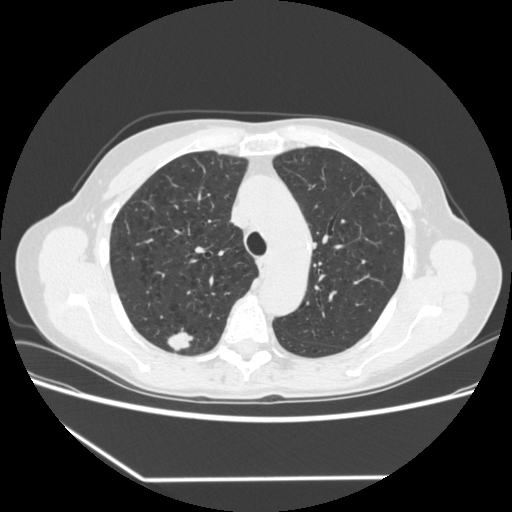
Chest CT (low-dose screening protocol), one axial image. First (baseline) screen. Lung window (W 1500 / L -600 HU). Slice 244 of 323 in the series. 512 × 512 image matrix. Female participant, aged 67 years at enrolment. Current smoker at enrolment.
Expert reader's lesion annotation, bounding box [x1, y1, x2, y2] px = [155, 323, 200, 358]. The screening reader recorded 2 non-calcified nodules or masses ≥4 mm on this exam (right upper lobe, right lower lobe); which of them this box marks is not recorded. Official screen result: positive, change unspecified: nodule(s) >= 4 mm or enlarging nodule(s), mass(es), or other non-specific abnormalities suspicious for lung cancer. Lung cancer was diagnosed 29 days after this screen: adenocarcinoma, NOS, right upper lobe, moderately differentiated (G2), stage IA (AJCC 6th edition), 24 mm at pathology.